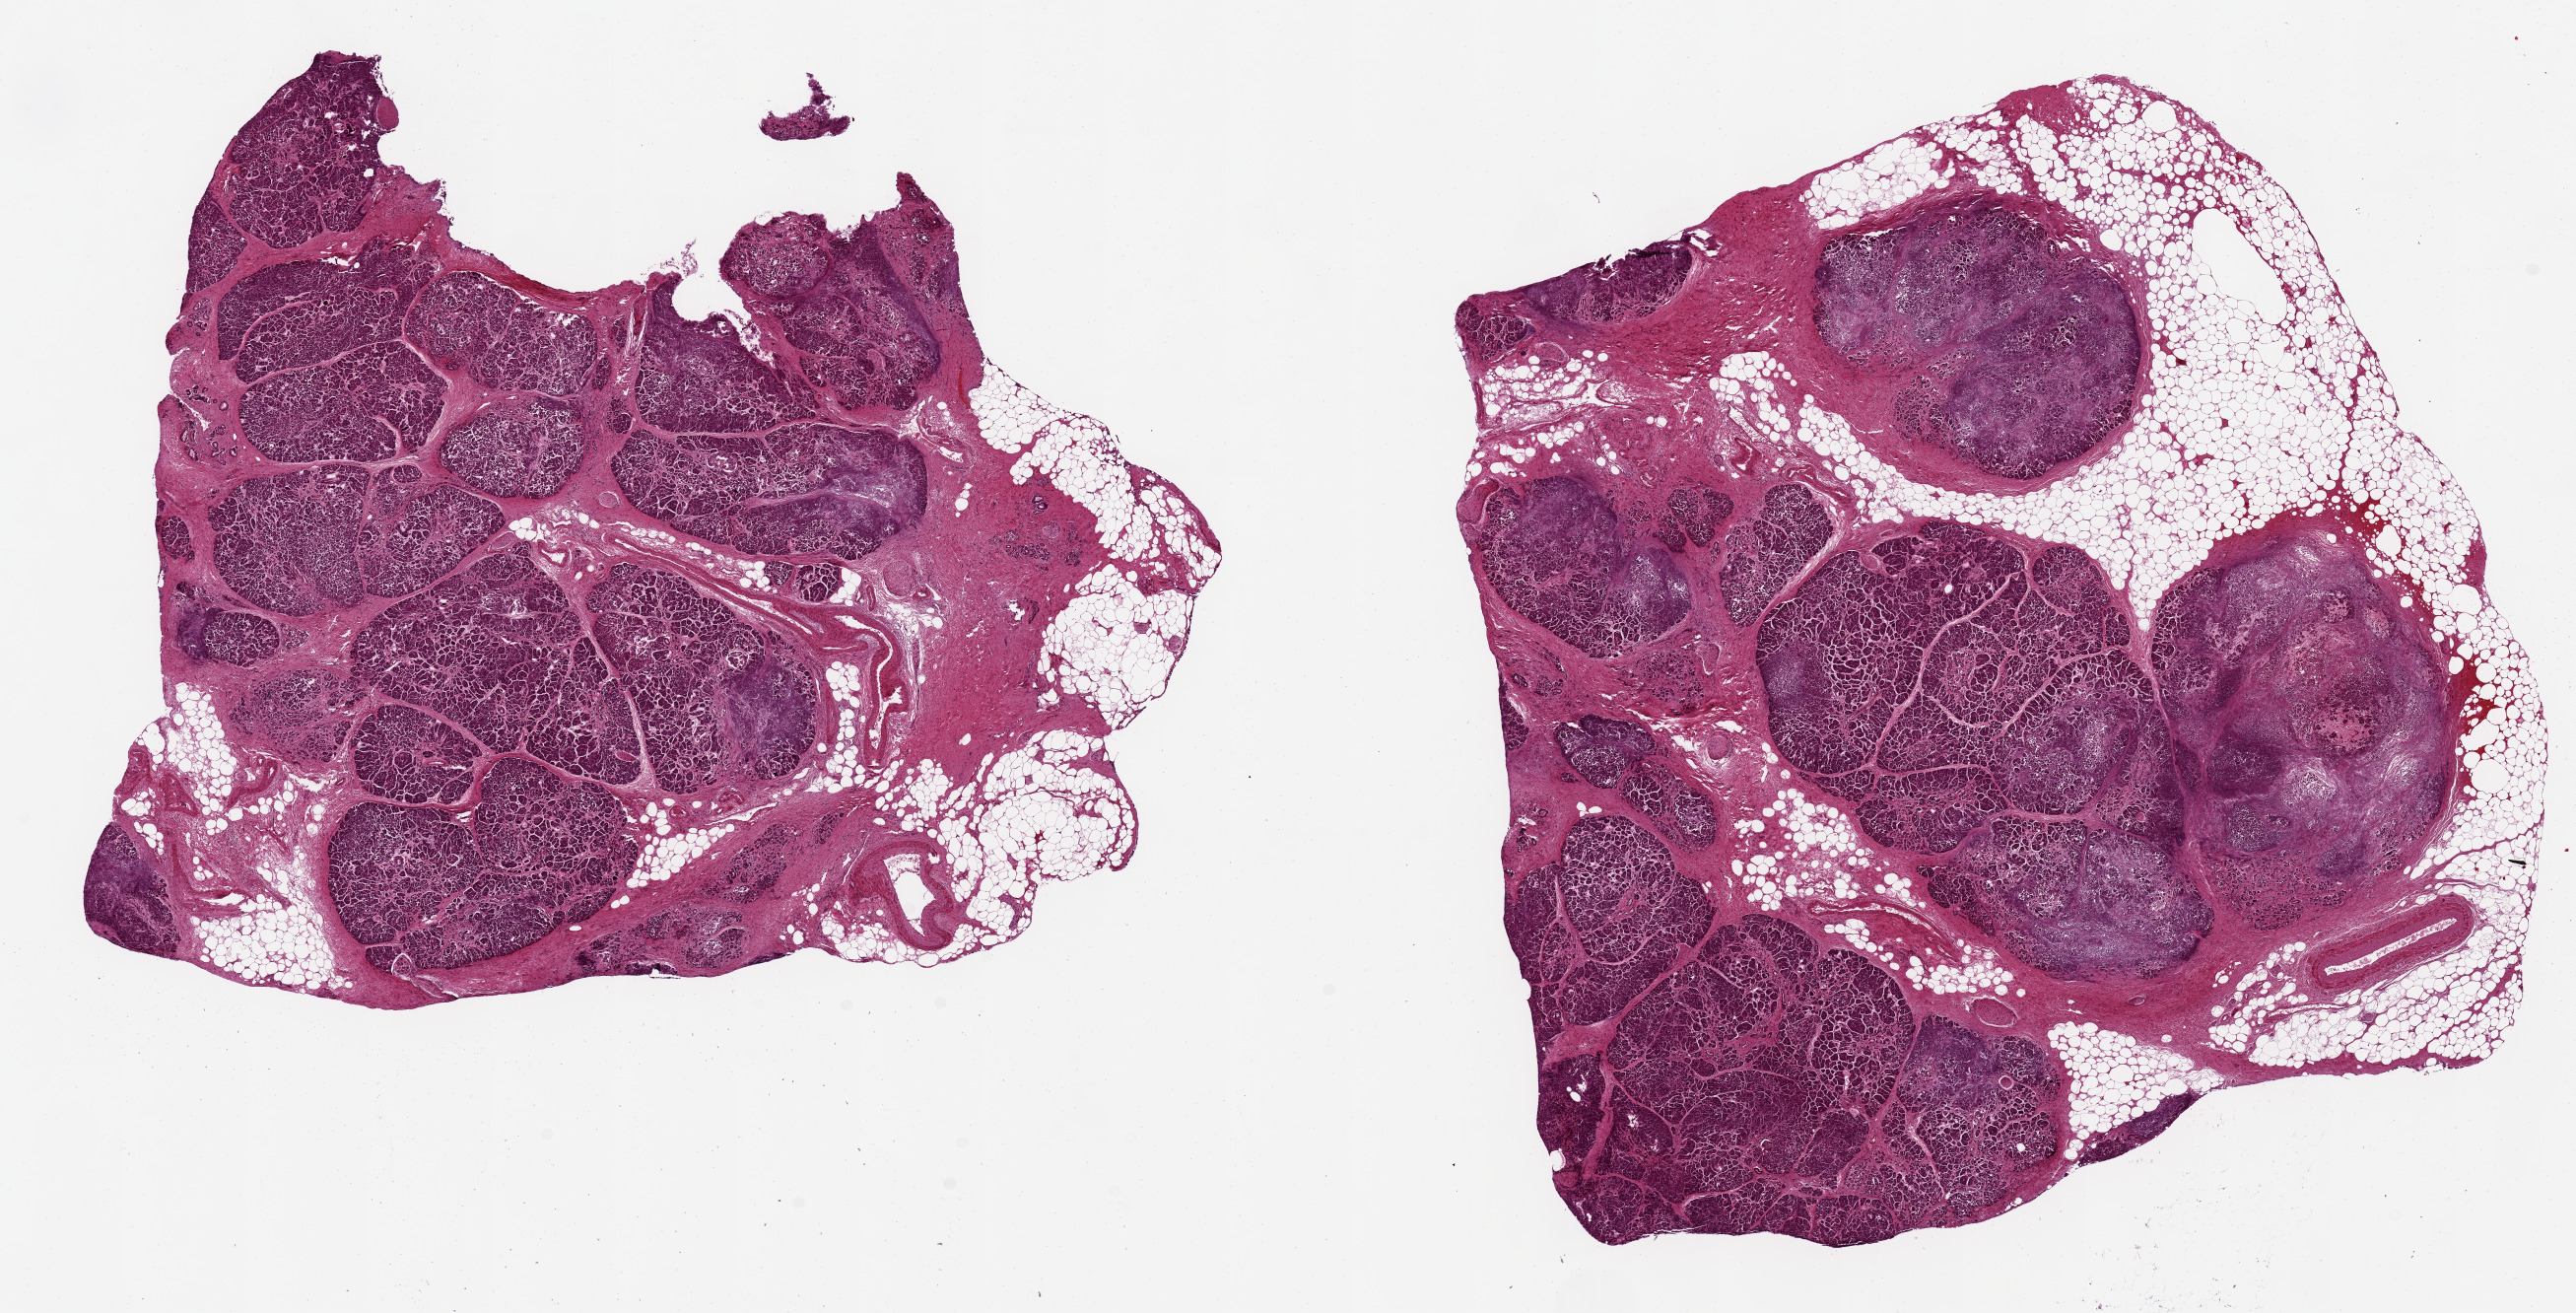
Haematoxylin and eosin whole-slide image, a low-resolution overview of the entire scanned area, about 20.7 x 10.5 mm; PAXgene-fixed, paraffin-embedded tissue; sampled site (target tissue): pancreas; tissue donor sample. Donor sex: male.
Reviewer comment on this tissue sample: 2 aliquots, ~8x8mm. ~40% adherent + interstitial fat, moderate-marked autolysis & saponification.